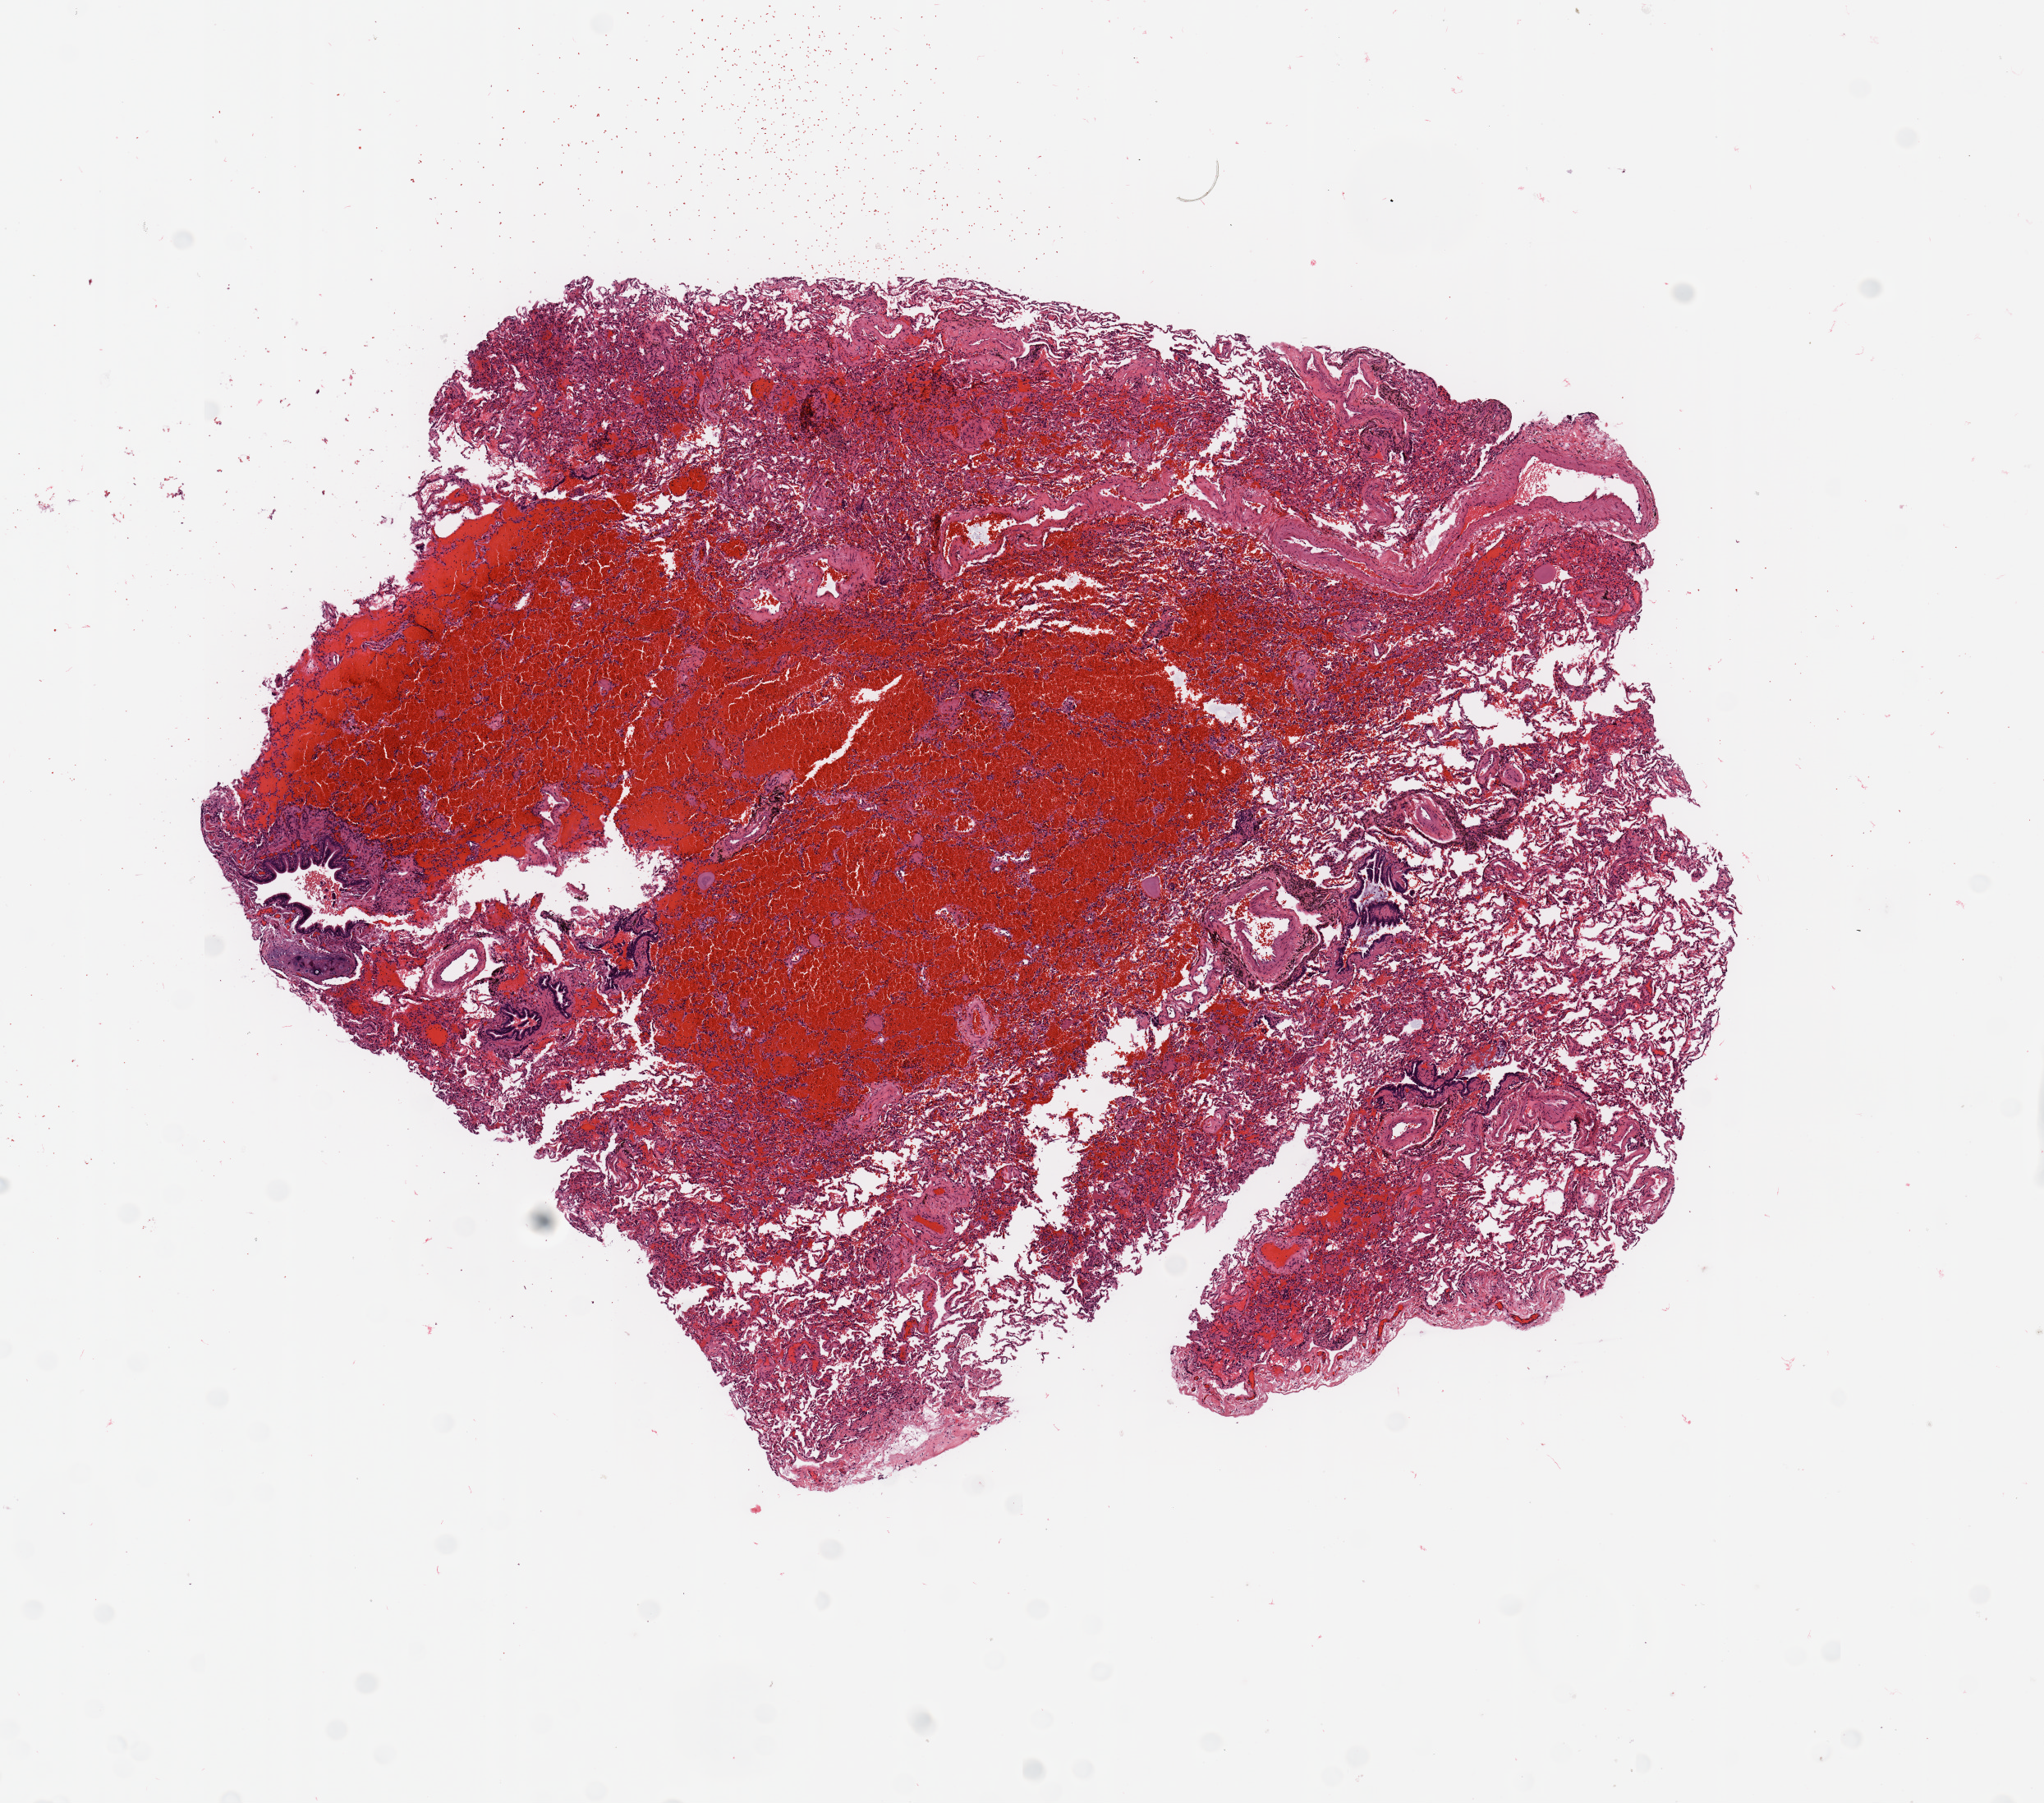
Digitized Hematoxylin and eosin (H&E) stained tissue section (whole slide), low-resolution overview of the scanned area, about 9.8 x 8.7 mm (from a 20x scan). Normal (non-tumour) tissue sample, sampled site: lung. Patient: male, age 65 years.
This section: normal (non-tumour) tissue from the same patient. Patient diagnosis: Adenocarcinoma, NOS.